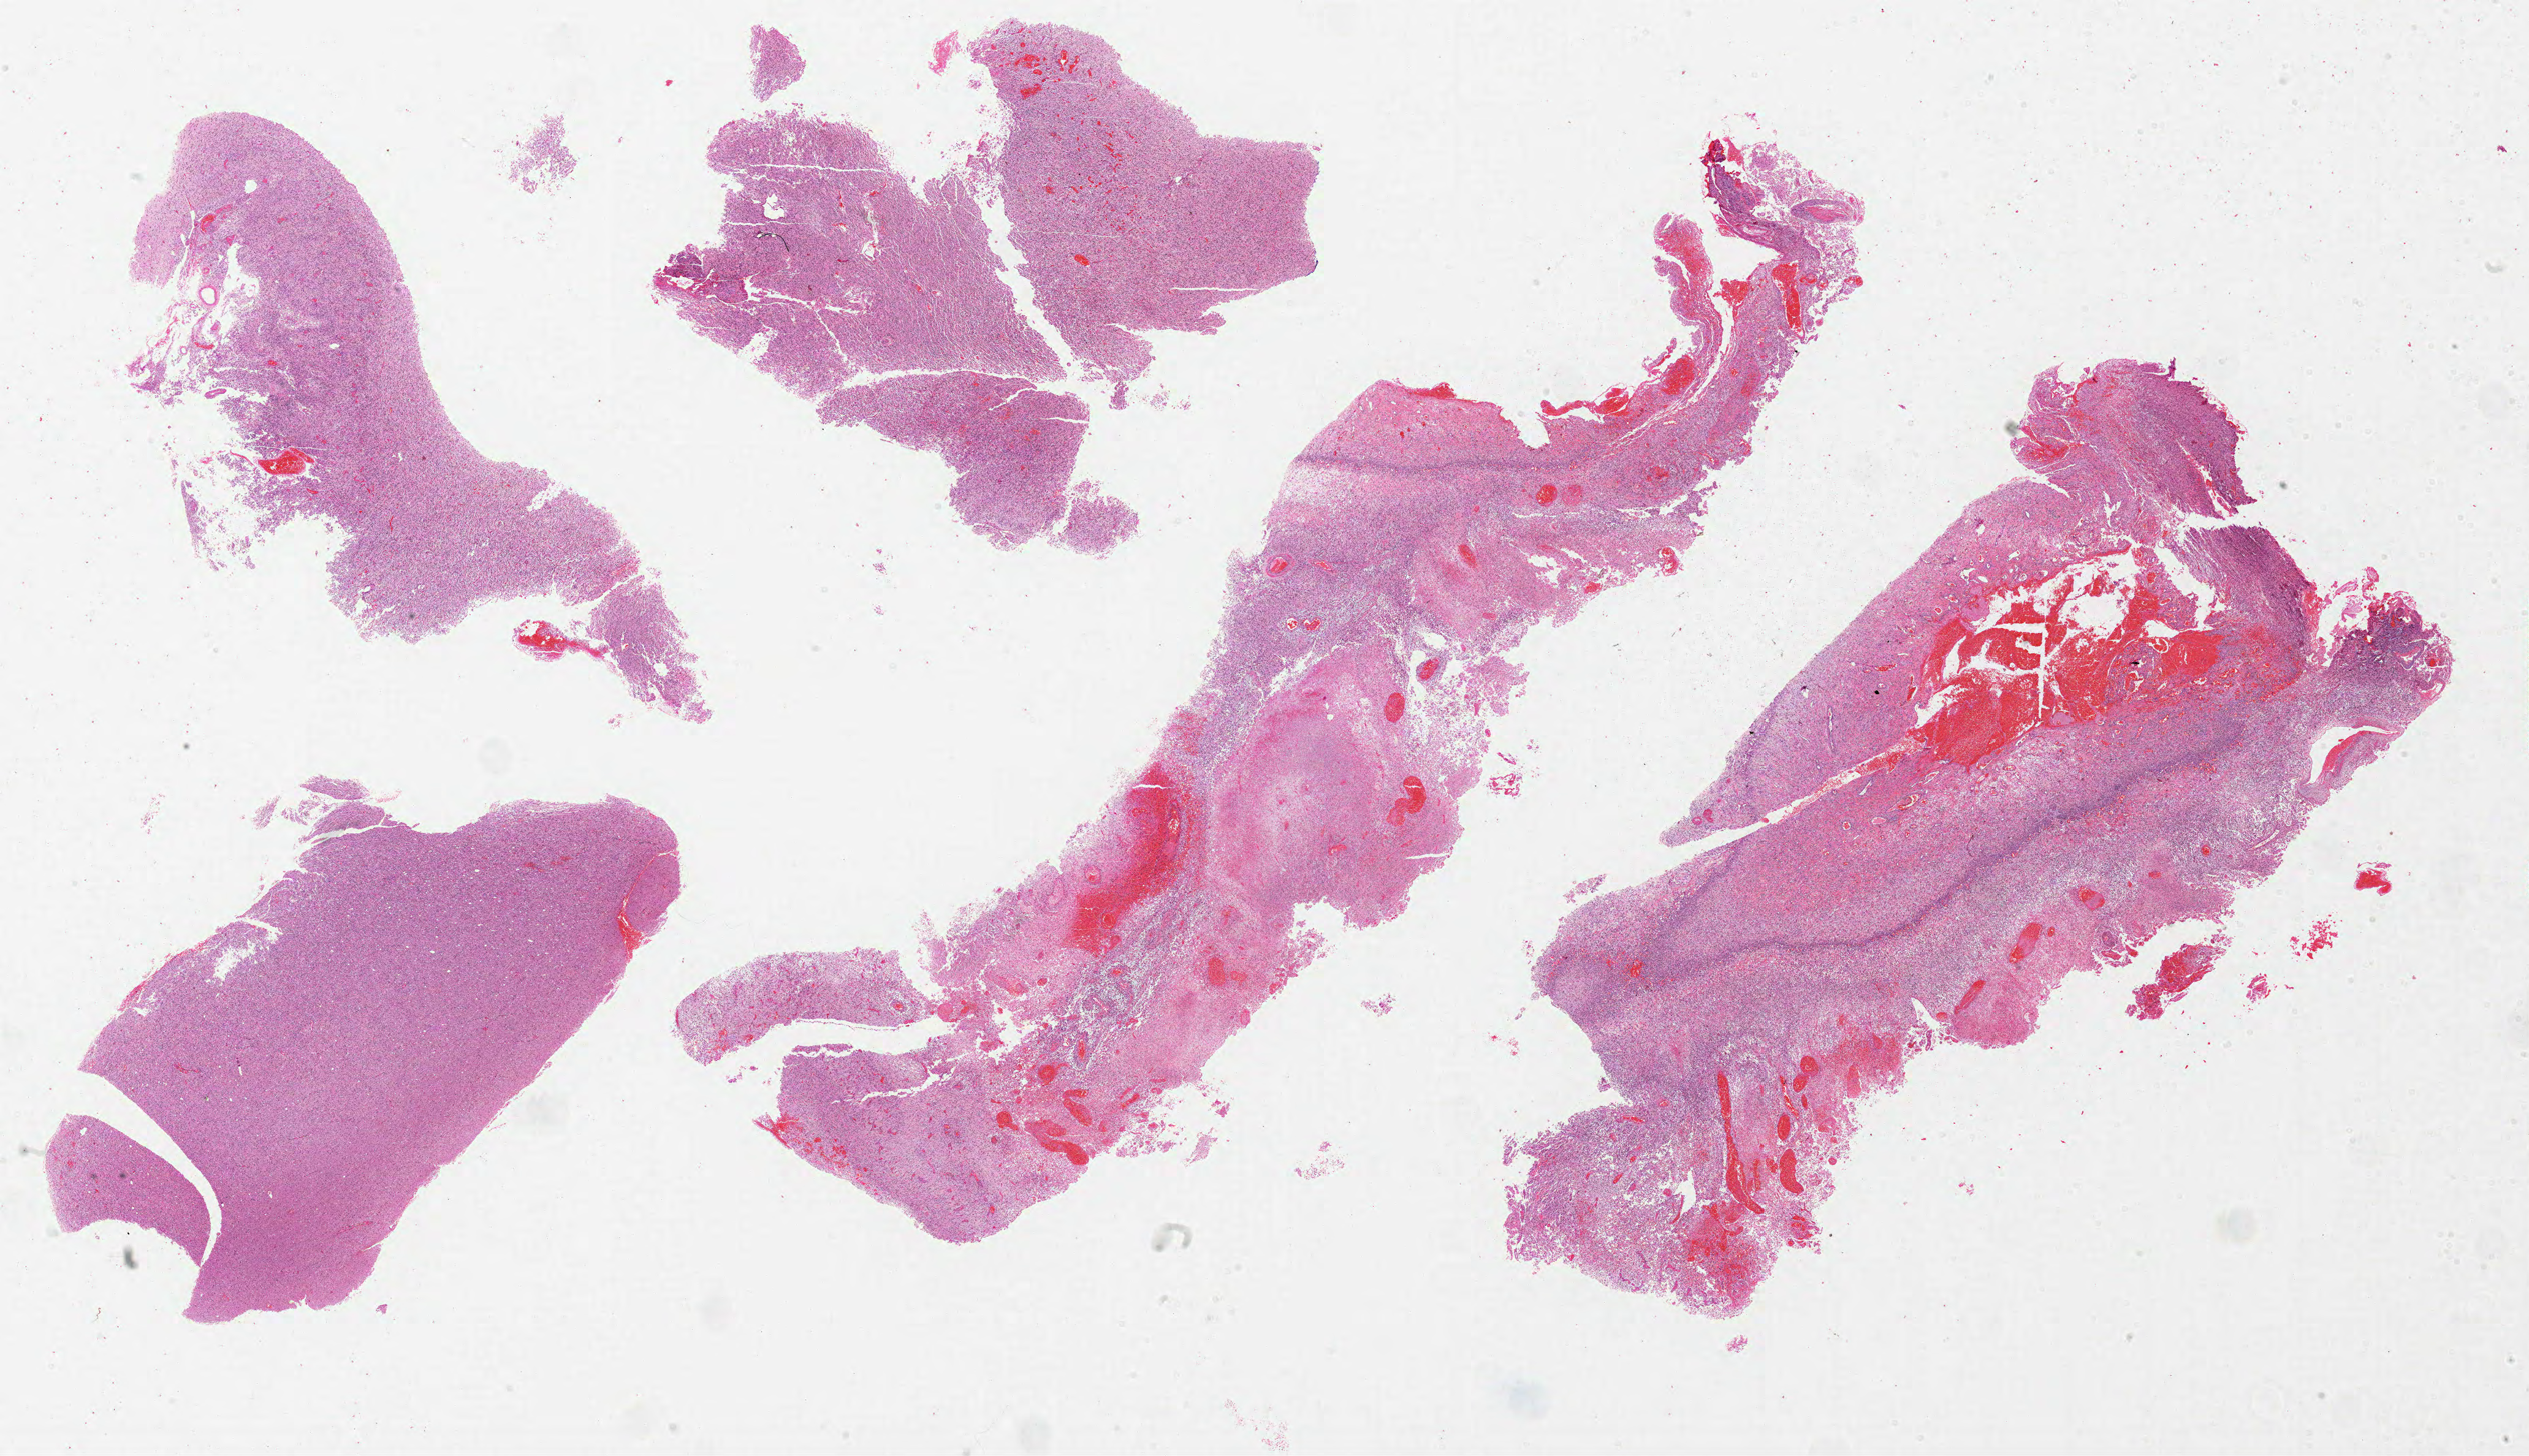
Digitized Hematoxylin and eosin (H&E) stained tissue section (whole slide), shown as a low-resolution overview of the whole scanned area (about 33.0 x 19.0 mm, acquisition: 20x scan); formalin-fixed paraffin-embedded (FFPE) diagnostic section; primary tumour sample from the brain. Patient: female, age at initial diagnosis 48 years.
Histologic diagnosis: Glioblastoma.